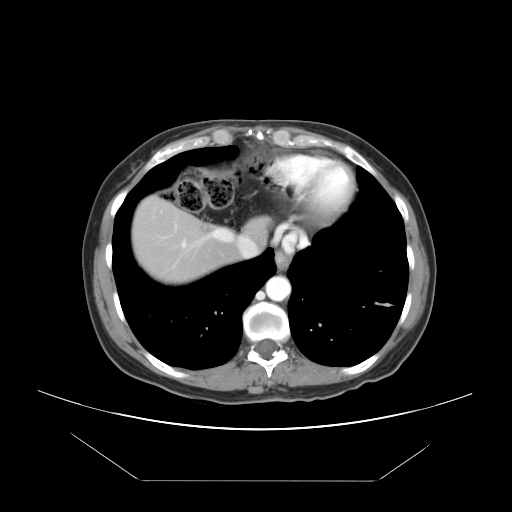
Contrast-enhanced abdominal CT, one axial slice; slice 40 of 45 in the series (ordered by position); reconstruction kernel STANDARD; 120 kVp; intravenous contrast given; soft-tissue window (W 400 / L 40 HU); 512 × 512 image matrix, field of view 405 × 405 mm. Female patient, age 52 years. From the clinical record (not read from this slice): diagnosis: colorectal cancer liver metastases, imaged before liver resection; multiple liver metastases: yes; largest metastasis: 2.5 cm; disease in both lobes: no.
Structures marked on this image (manually delineated by an expert):
- hepatic veins: bounding box [x1, y1, x2, y2] px = [160, 210, 256, 263]
- liver: [133, 199, 265, 280]
- planned liver remnant (the part of the liver to remain after resection): [133, 199, 265, 277]